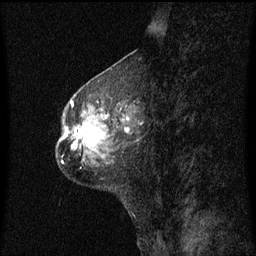
Breast MRI (dynamic contrast-enhanced), one sagittal slice; slice 22 of 60 in the series (ordered by position); dynamic contrast-enhanced series, image 2 of 3 at this slice position (ordered by acquisition); 1.5 T; TE 4.2 ms, TR 8.4 ms; 256 × 256 image matrix, field of view 200 × 200 mm. Female patient, age 49 years. Case-level facts recorded for this patient, not image findings: setting: breast cancer imaged before/during neoadjuvant chemotherapy; receptor status: HR-positive, HER2-negative.
Outlined on this slice (semi-automatic segmentation, software-assisted and operator-edited):
- analysis volume of interest (the breast-tissue region the enhancement analysis was run in; not a lesion): bounding box [x1, y1, x2, y2] px = [59, 101, 138, 158]
- tumour enhancement mask (voxels above the 70 % enhancement threshold inside the analysis volume of interest): [70, 116, 130, 149]